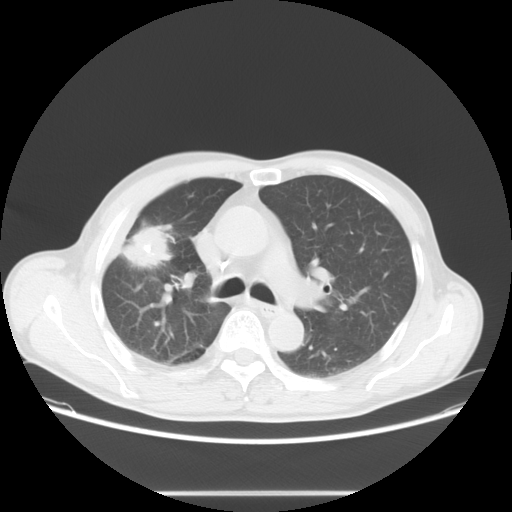
Chest CT, one axial slice. Reconstruction kernel STANDARD. Lung window (W 1500 / L -600 HU). 5 mm slice thickness. 512 × 512 image matrix, field of view 392 × 392 mm. Male patient, age 67 years. From the clinical record (not read from this slice): clinical TNM (as recorded): T2 N0 M0.
Outlined on this slice (rectangle marked by the reading radiologist):
- lung tumour (recorded histology: adenocarcinoma): bounding box <122,223,170,270> (left, top, right, bottom; pixels)